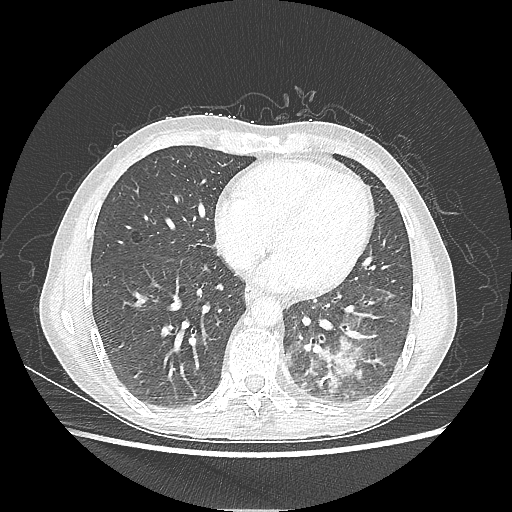
Chest CT, one axial slice. Slice 83 of 220 in the series (ordered by position). Lung window (W 1500 / L -600 HU). 1.25 mm slice thickness. 512 × 512 image matrix, field of view 360 × 360 mm. Female patient, age 53 years. Case-level facts recorded for this patient, not image findings: clinical TNM (as recorded): T3 N0 M0.
Structures marked on this image (bounding box drawn by a radiologist):
- lung tumour (recorded histology: adenocarcinoma): box from (x=303, y=331) to (x=365, y=392) px